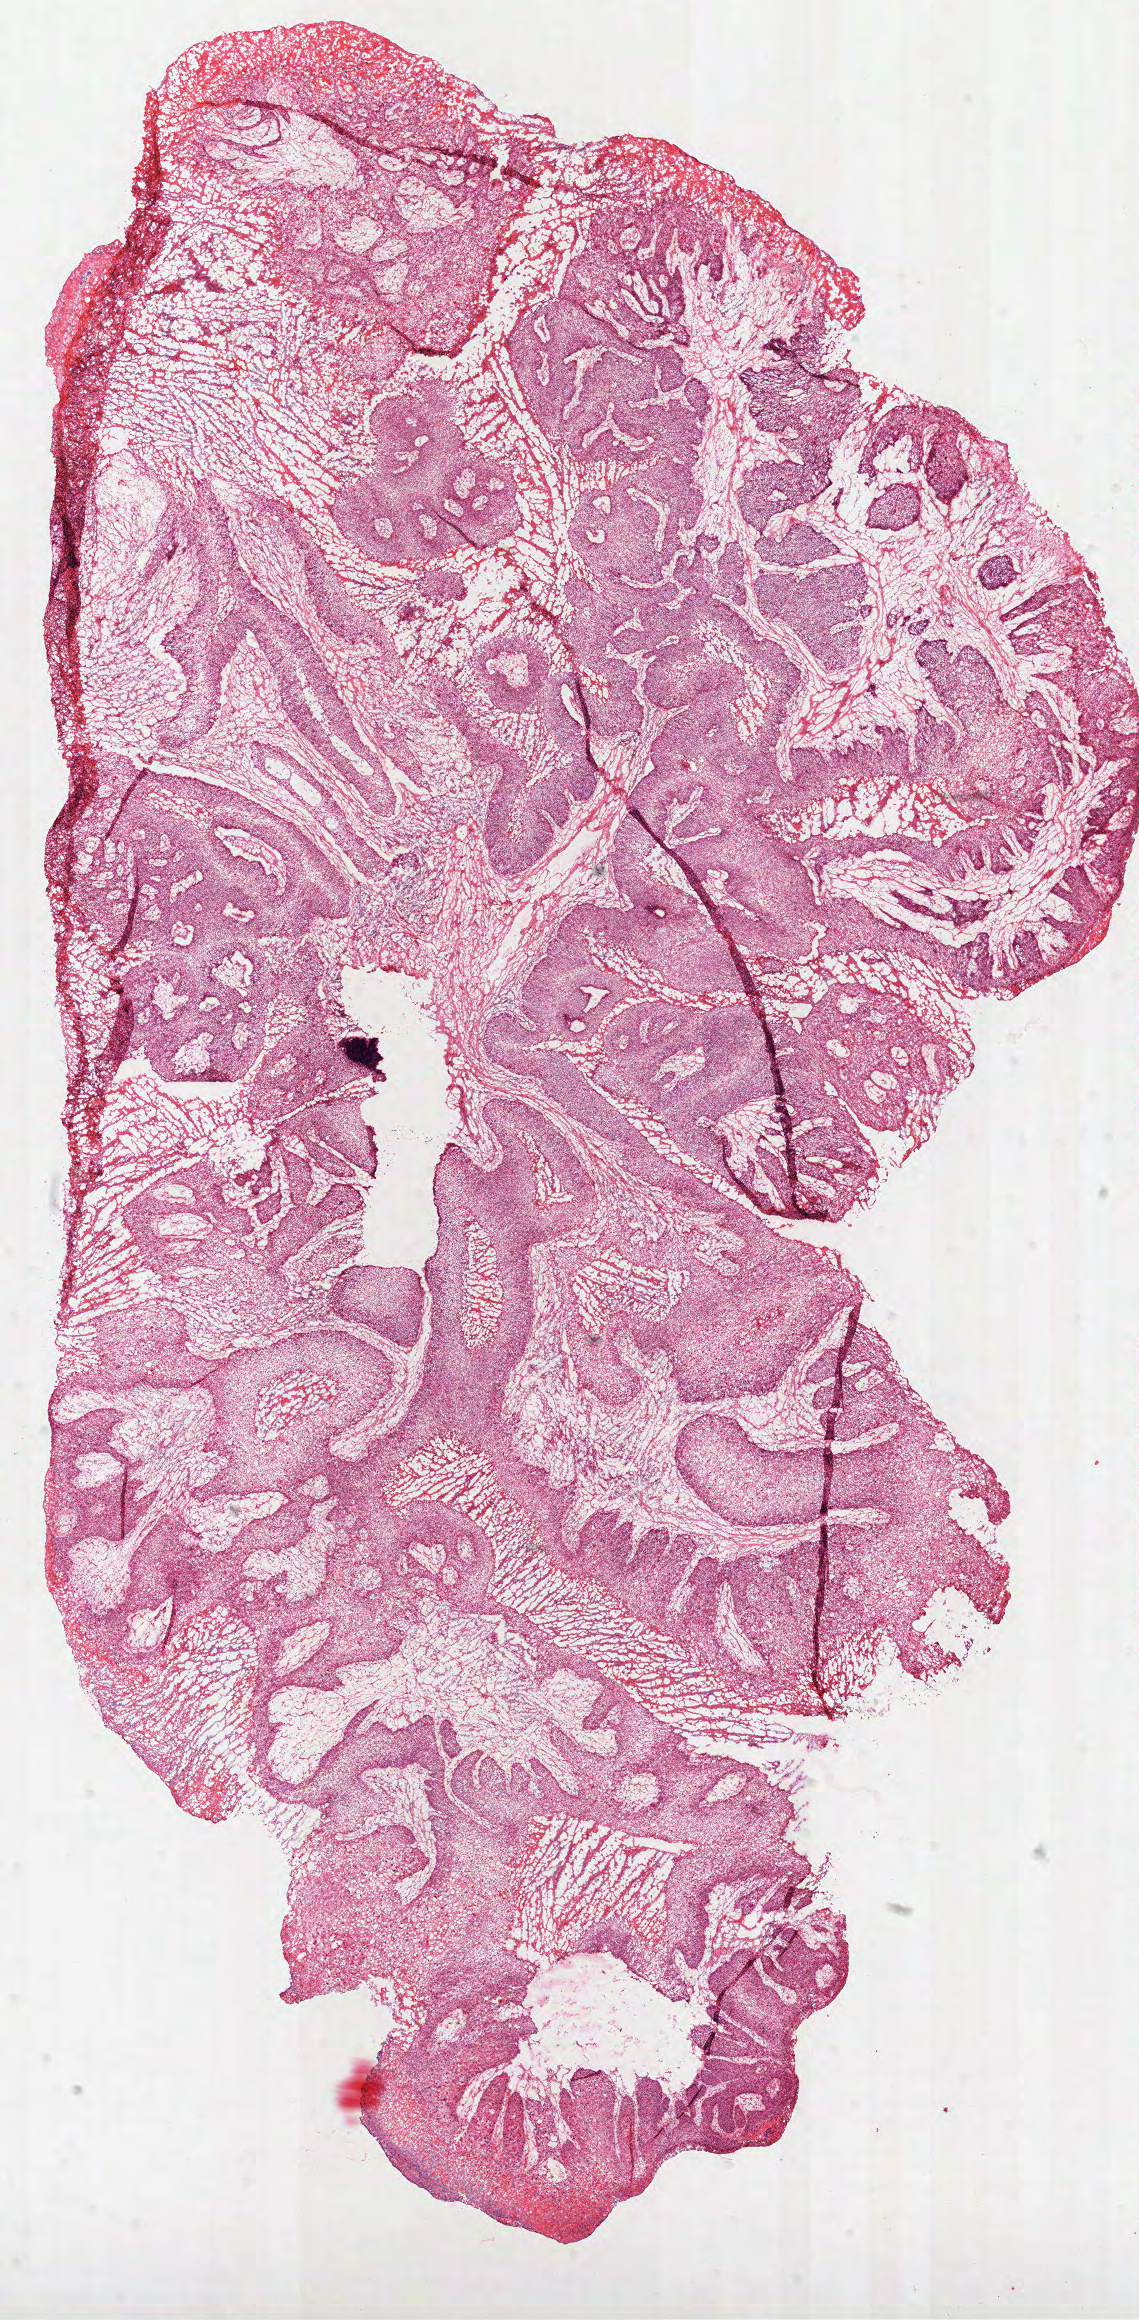
Whole-slide histology image, H&E-stained — a low-resolution overview of the entire scanned area, about 9.2 x 18.7 mm (from a 40x scan). Frozen section from the top of the tissue portion. Sample: primary tumour, lung. Male patient; age at initial diagnosis 66 years. Pathologist review of this section (percent, as recorded): tumour cells 80%, tumour nuclei 75%, normal cells 0%, stromal cells 15%, necrosis 5%. Infiltration values recorded for this section: lymphocyte infiltration 10%, neutrophil infiltration 10%.
Laterality: left. Diagnosis: Papillary squamous cell carcinoma (lower lobe, lung). AJCC pathologic stage: IA (7th edition).